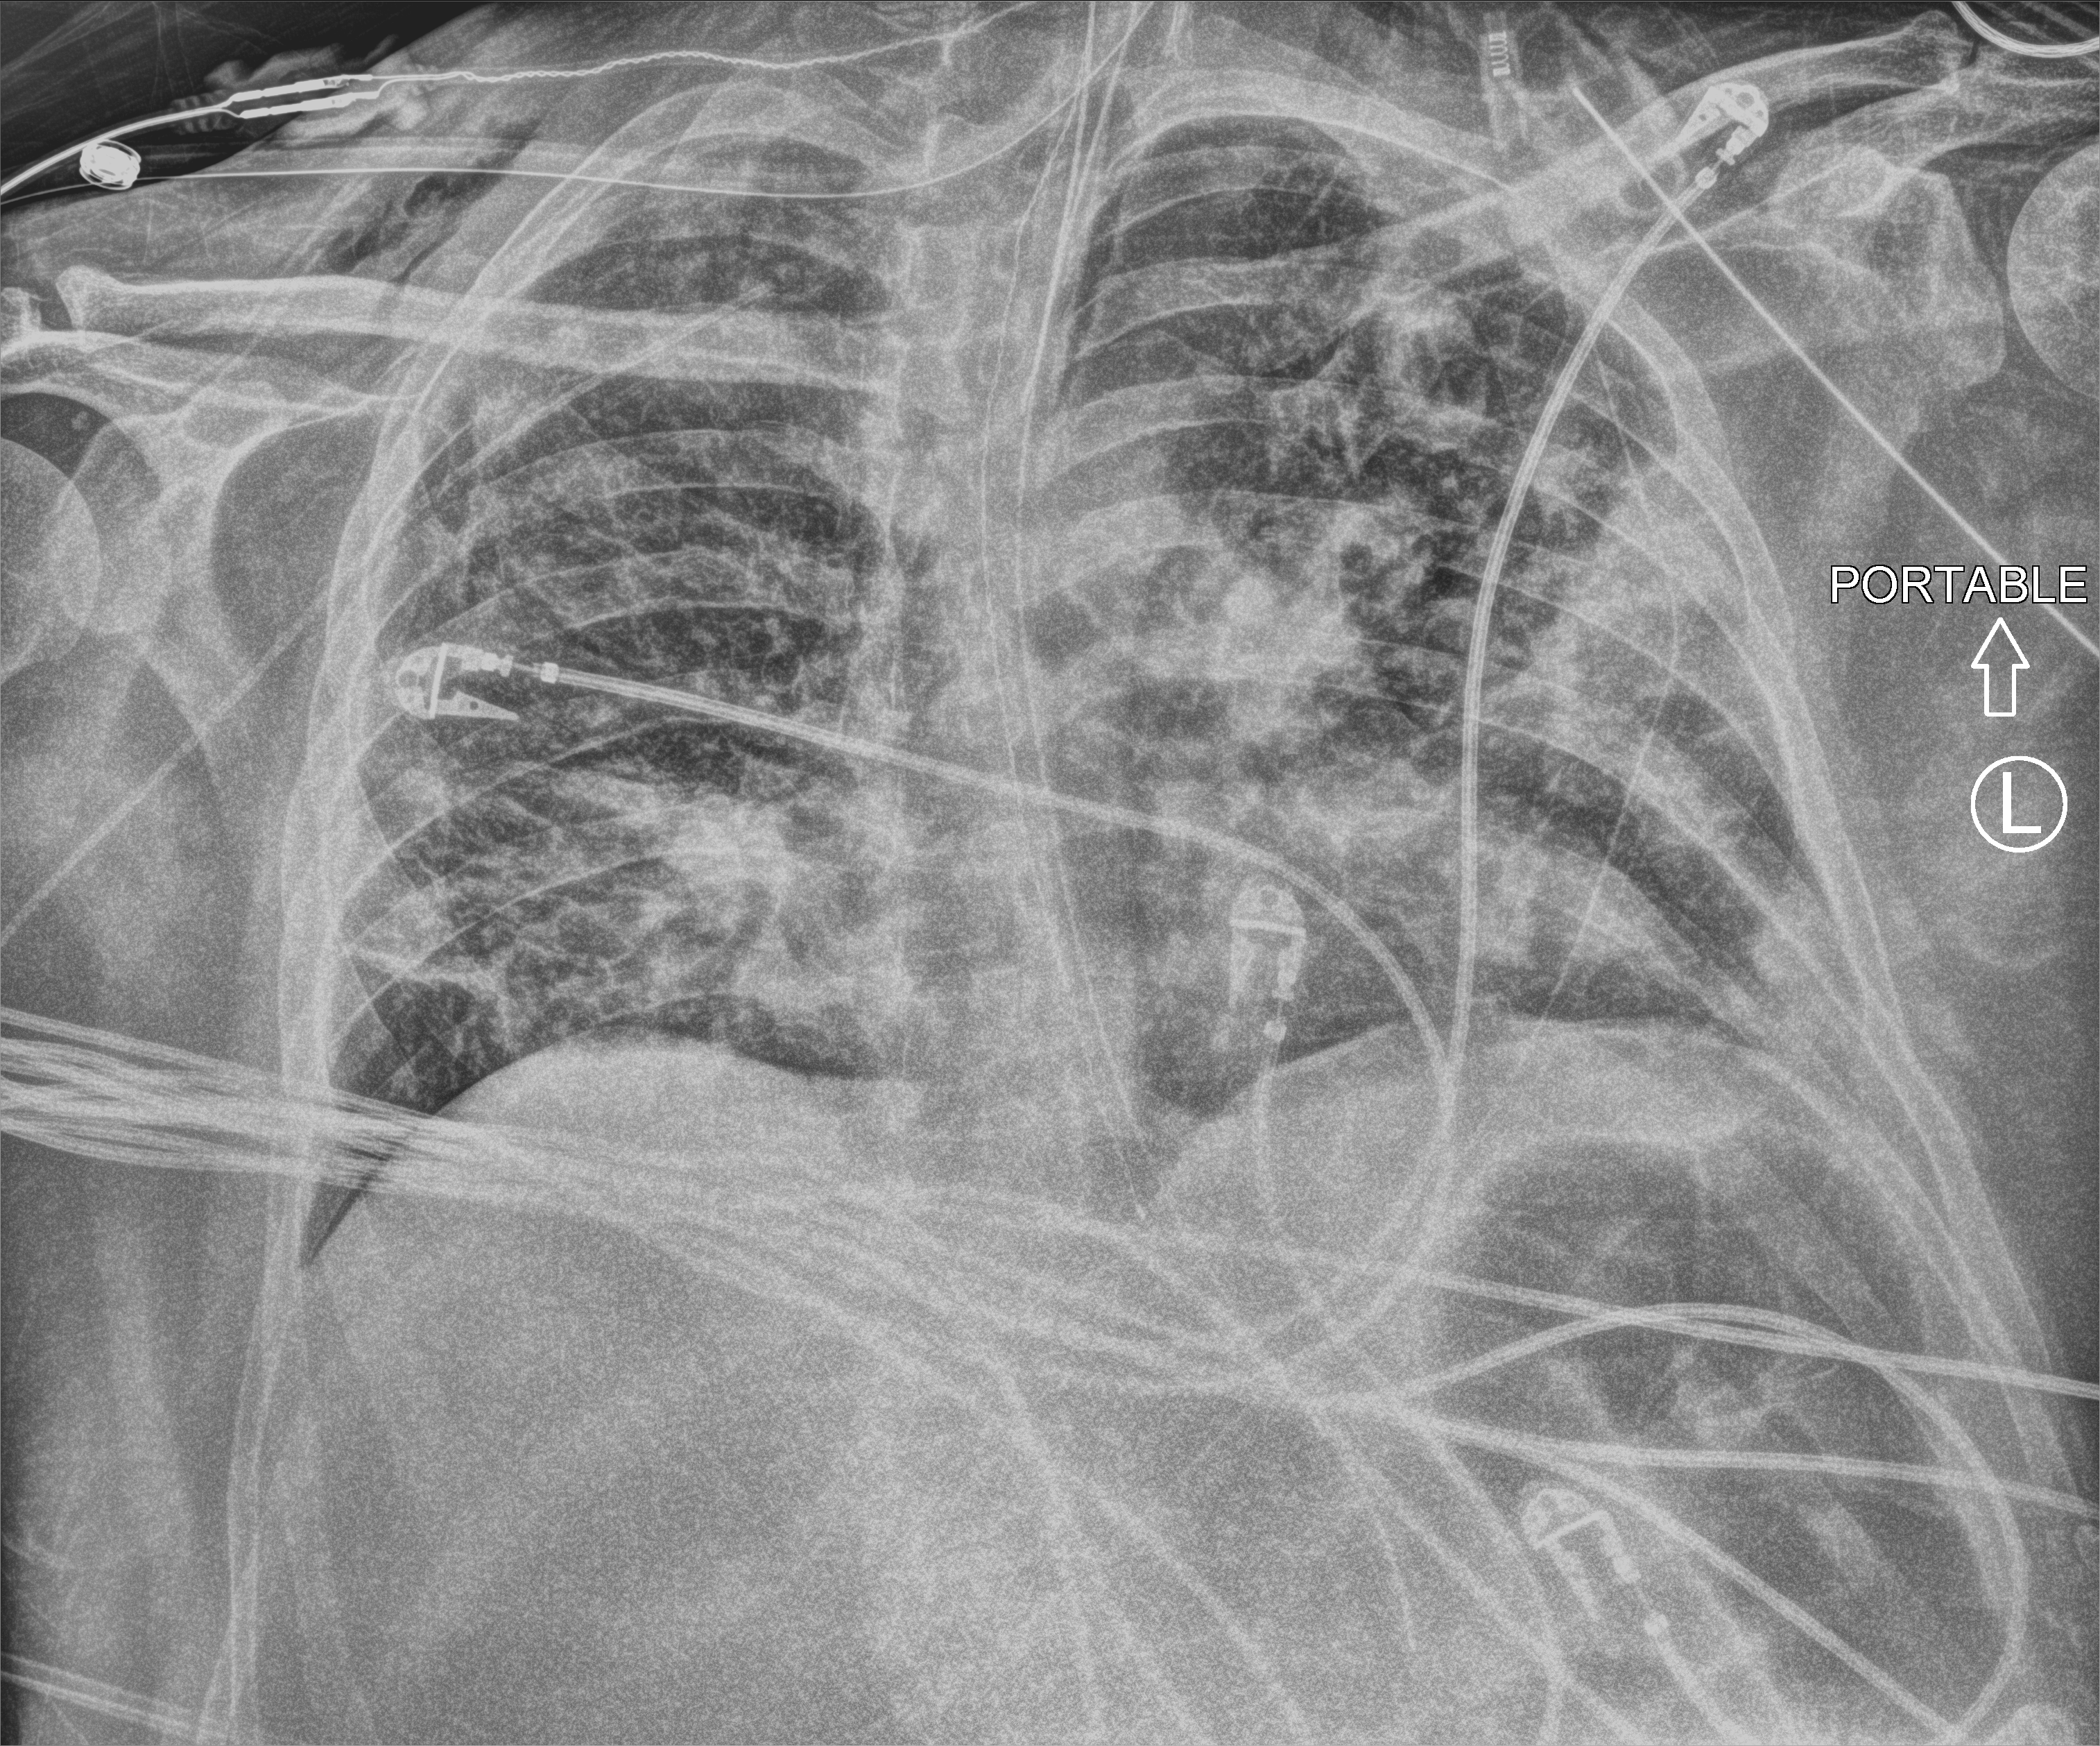
Chest X-ray (portable); anteroposterior (AP) projection. Adult patient hospitalised with COVID-19, age 18–59 years.
Hospital-stay facts (about this admission, not read from this image; timing relative to this image not recorded):
- other chronic lung disease (admission record): yes
- mechanically ventilated during this hospital stay: yes